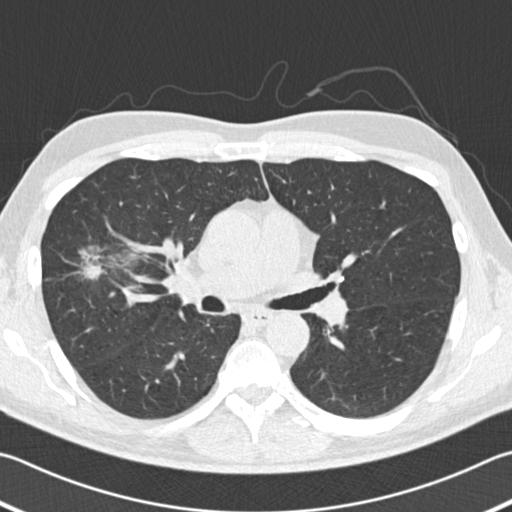
Low-dose screening chest CT, one axial slice; position 112 of 182 along the scan axis; reconstruction kernel B30f; lung window (W 1500 / L -600 HU); 2 mm slice thickness; 512 × 512 image matrix, field of view 344 × 344 mm.
Structures marked on this image (manually delineated by an expert):
- lesion 1 (tumor, upper lobe of right lung): bounding box [x1, y1, x2, y2] px = [79, 244, 127, 280]